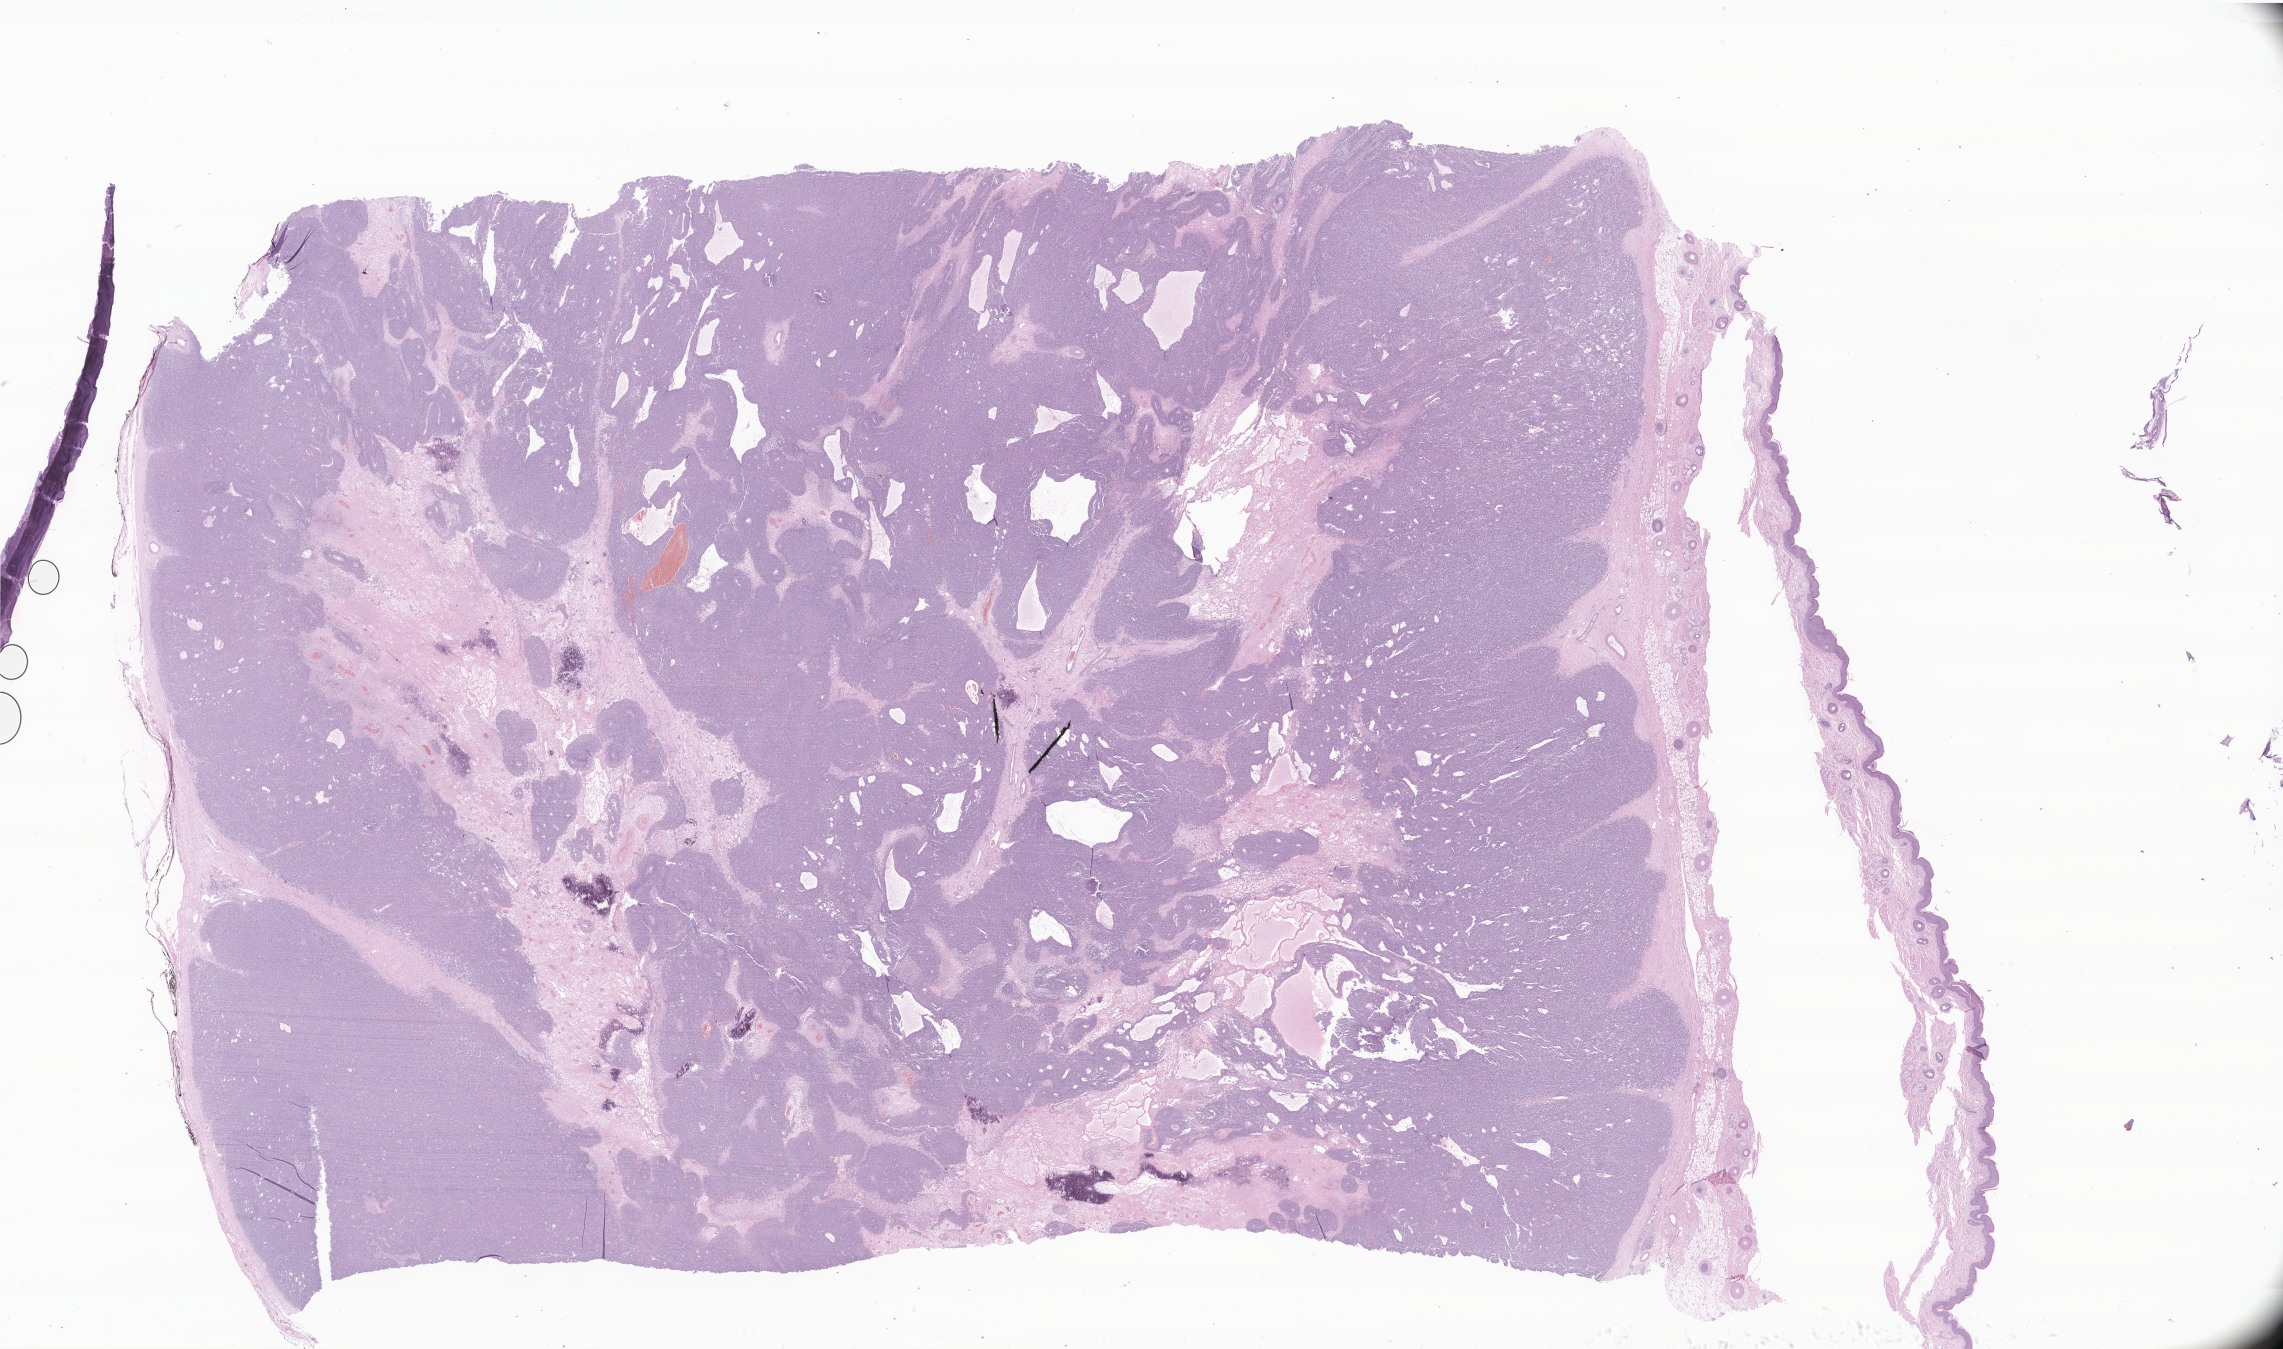
Whole-slide image, hematoxylin and eosin (H&E) stain of tumor tissue from the soft tissues of head and neck — whole scanned area (about 38.5 x 22.8 mm) shown as a low-resolution overview. Formalin-fixed, paraffin-embedded (FFPE) tissue. Patient: male, age 116 days.
- diagnosis (ICD-O-3 morphology term): Ewing sarcoma
- tissue or organ of origin (case record): connective, subcutaneous and other soft tissues of head, face, and neck